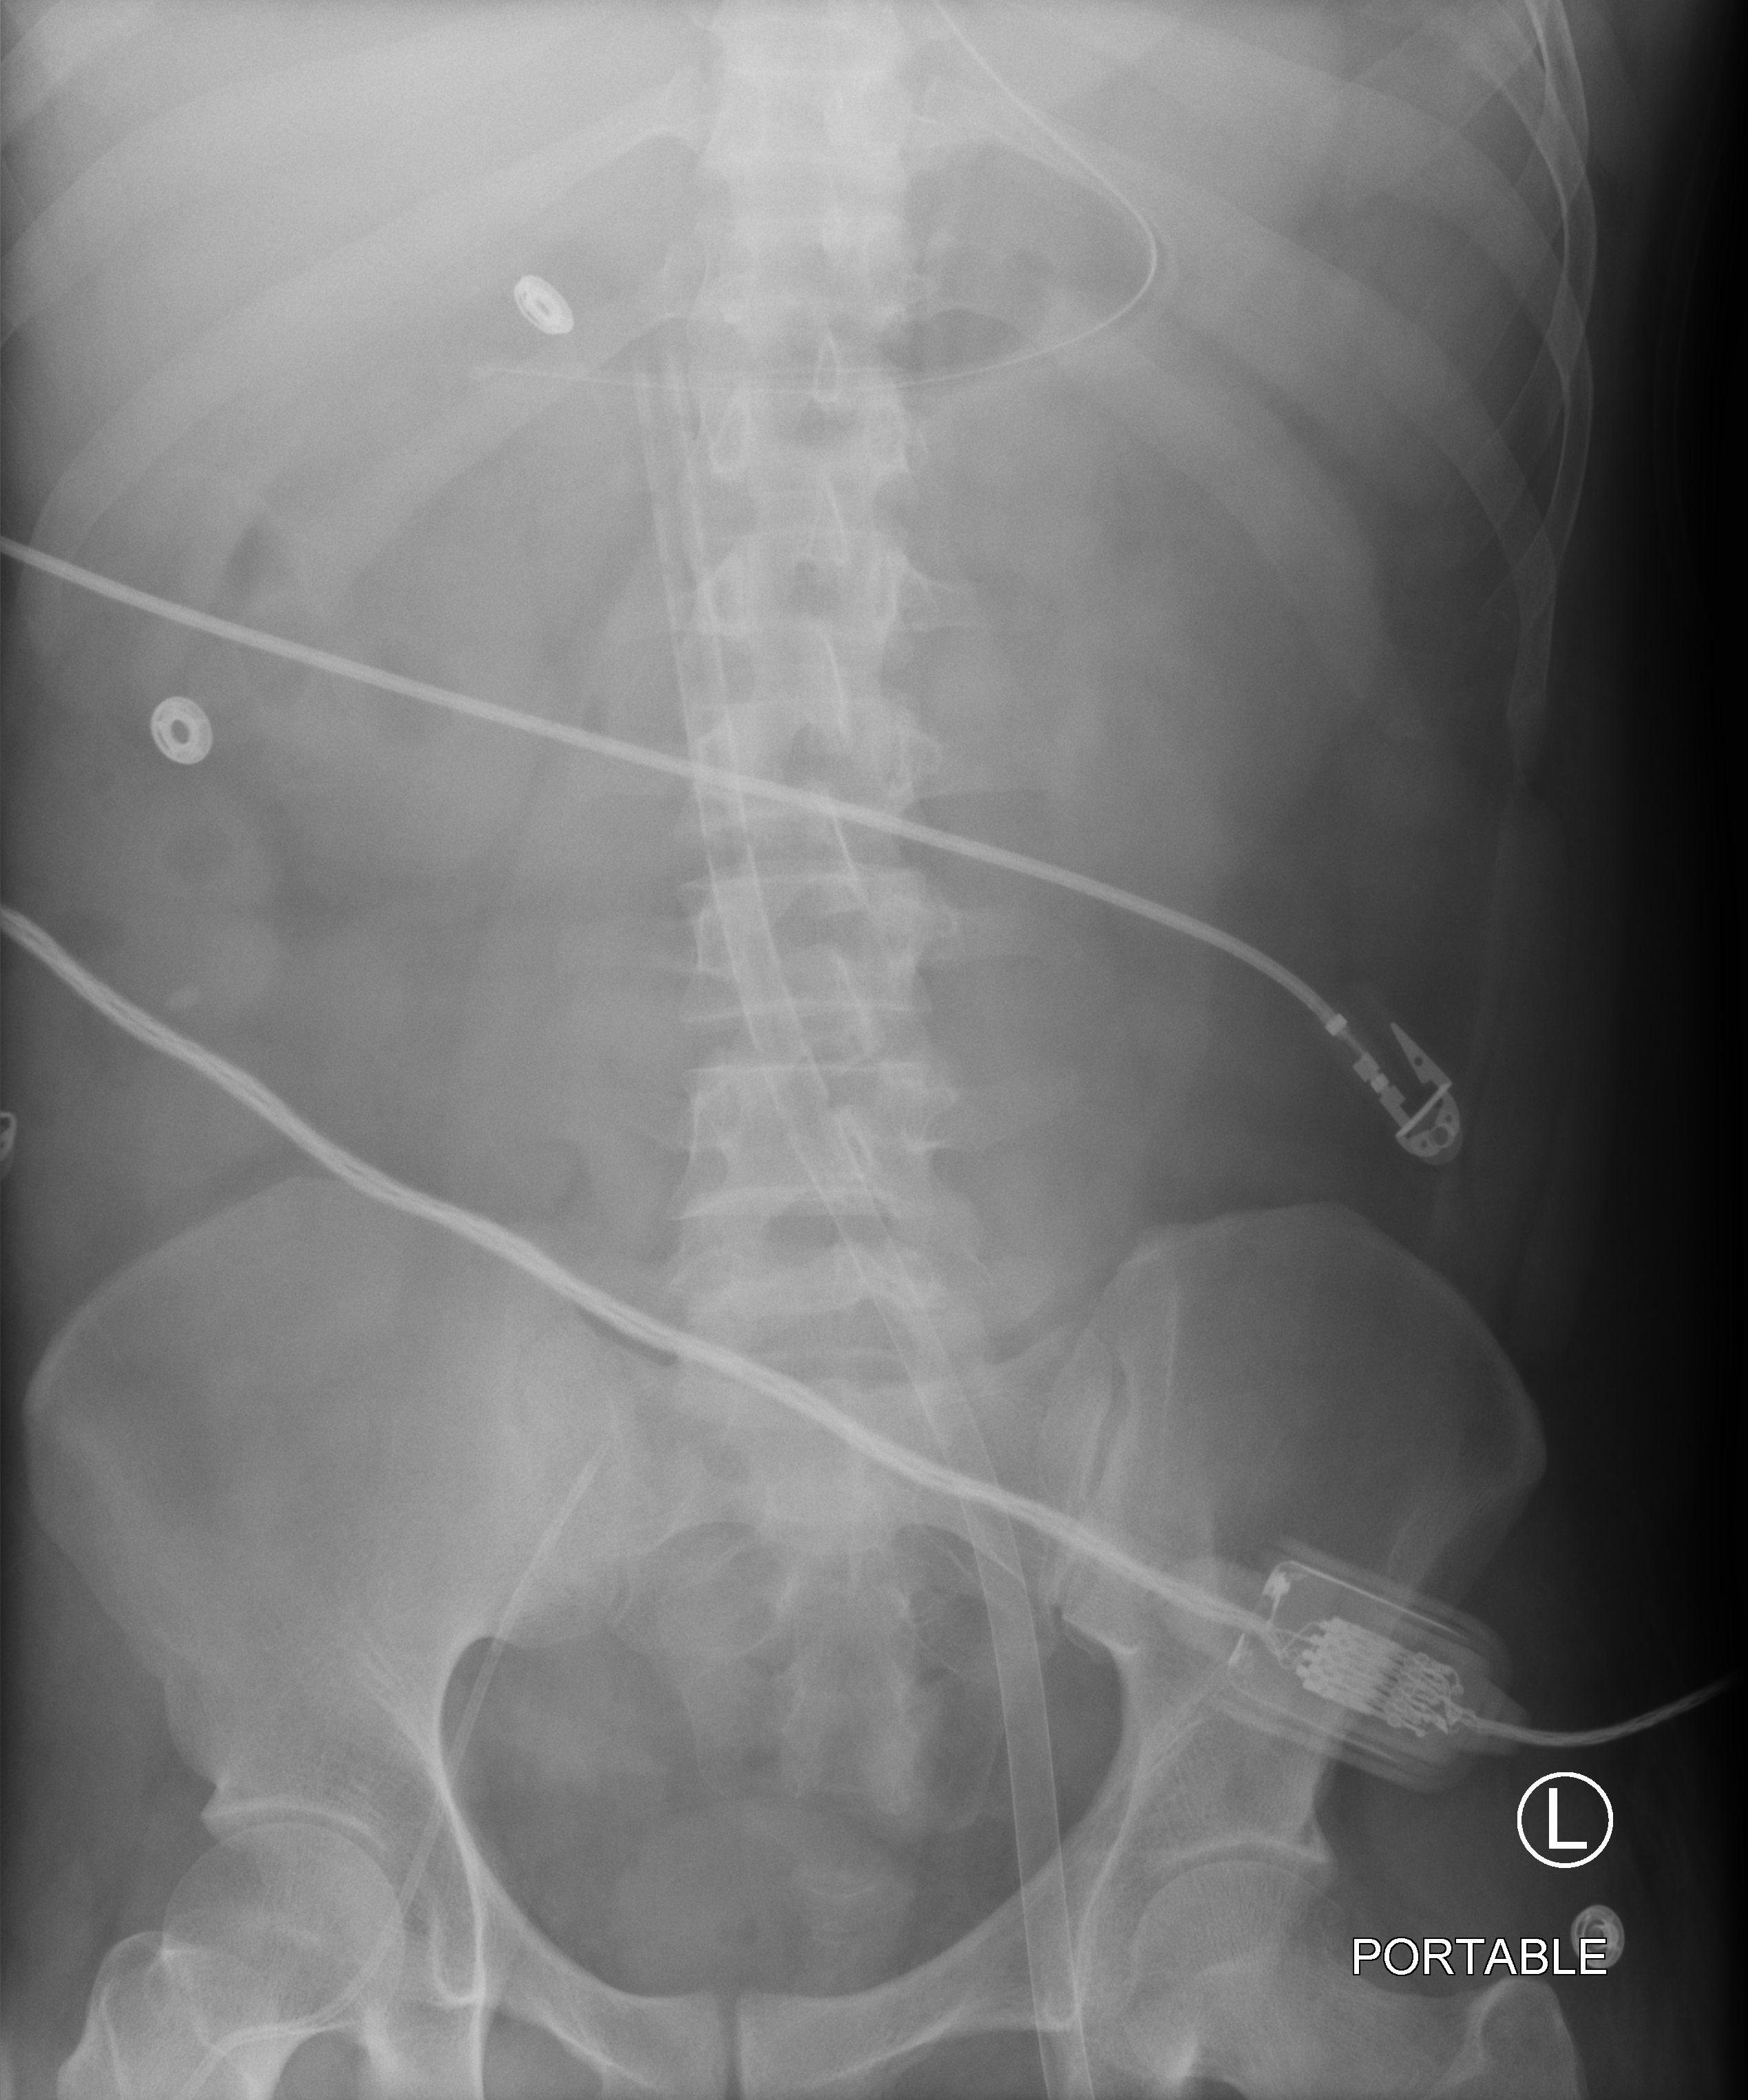
Bedside abdomen radiograph (computed radiography); anteroposterior (AP) projection. Adult patient hospitalised with COVID-19, age 18–59 years.
Hospital-stay facts (about this admission, not read from this image; timing relative to this image not recorded): smoking status (admission record): never; mechanically ventilated during this hospital stay: yes.